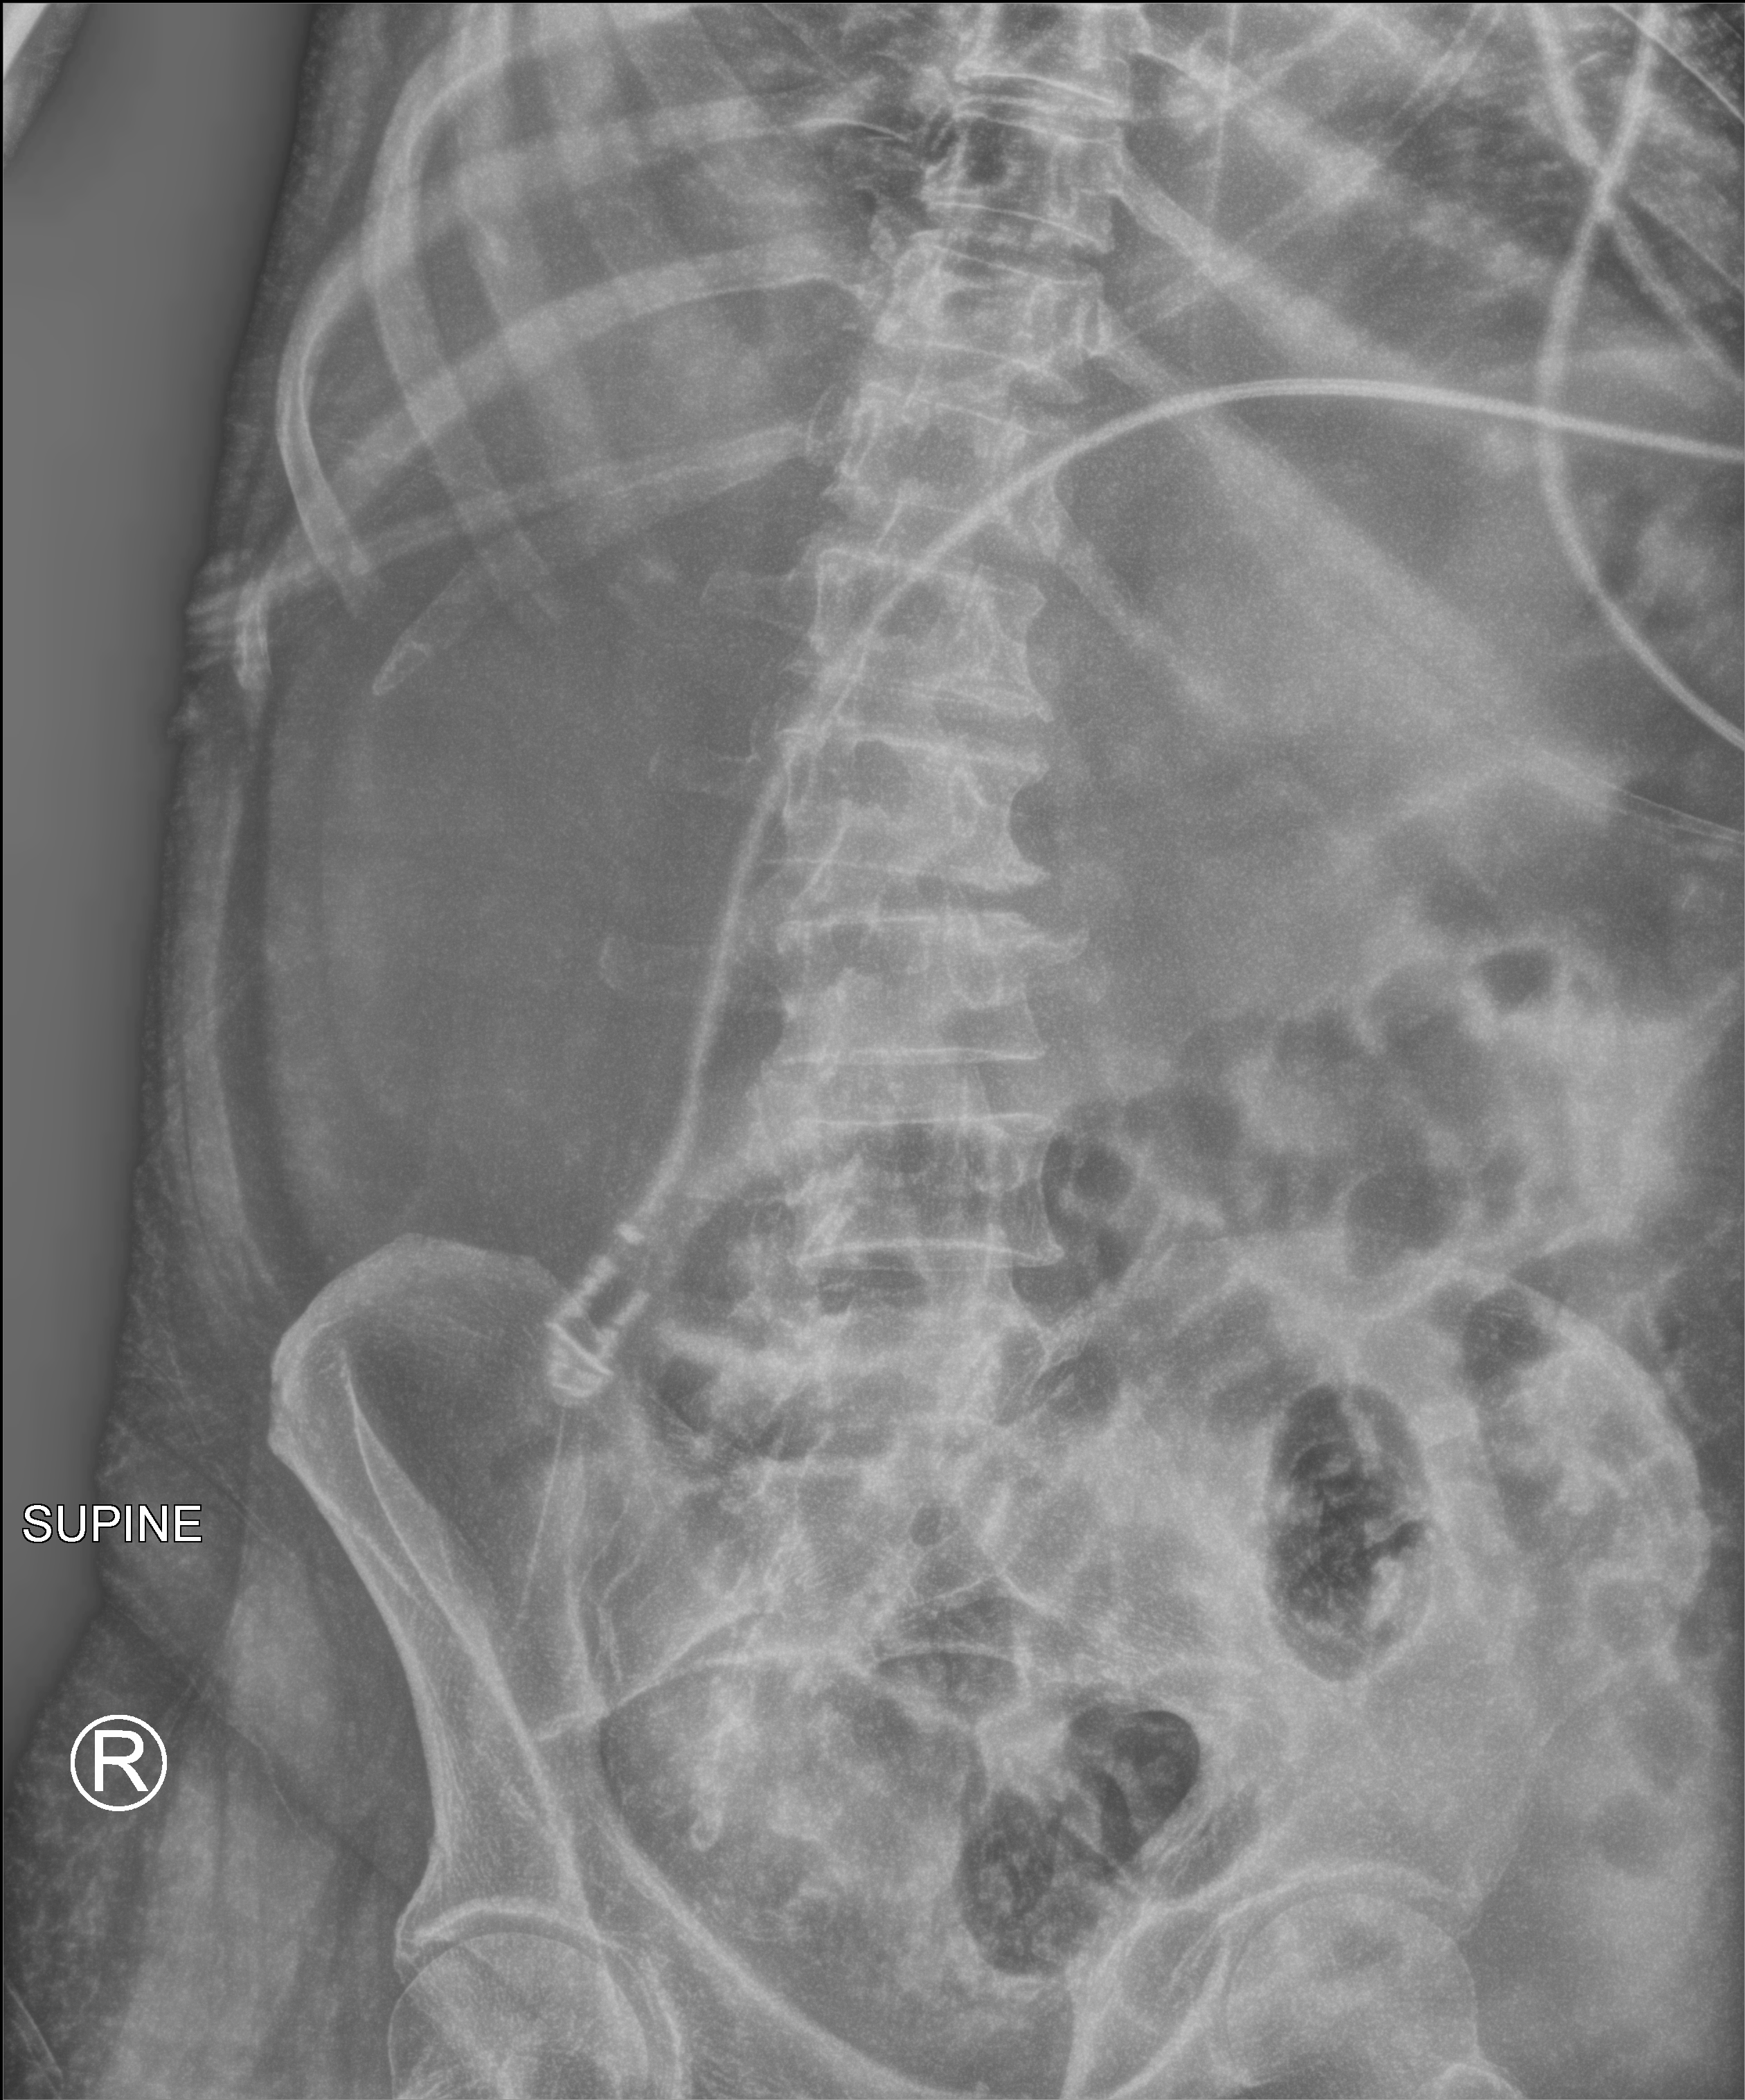
Bedside abdomen radiograph (computed radiography); anteroposterior (AP) projection. Male patient hospitalised with COVID-19, age 75–90 years.
From the hospital-stay record, not from the radiograph (when in the stay this image was taken is not recorded): mechanically ventilated during this hospital stay: yes; admitted to intensive care during this hospital stay: yes.